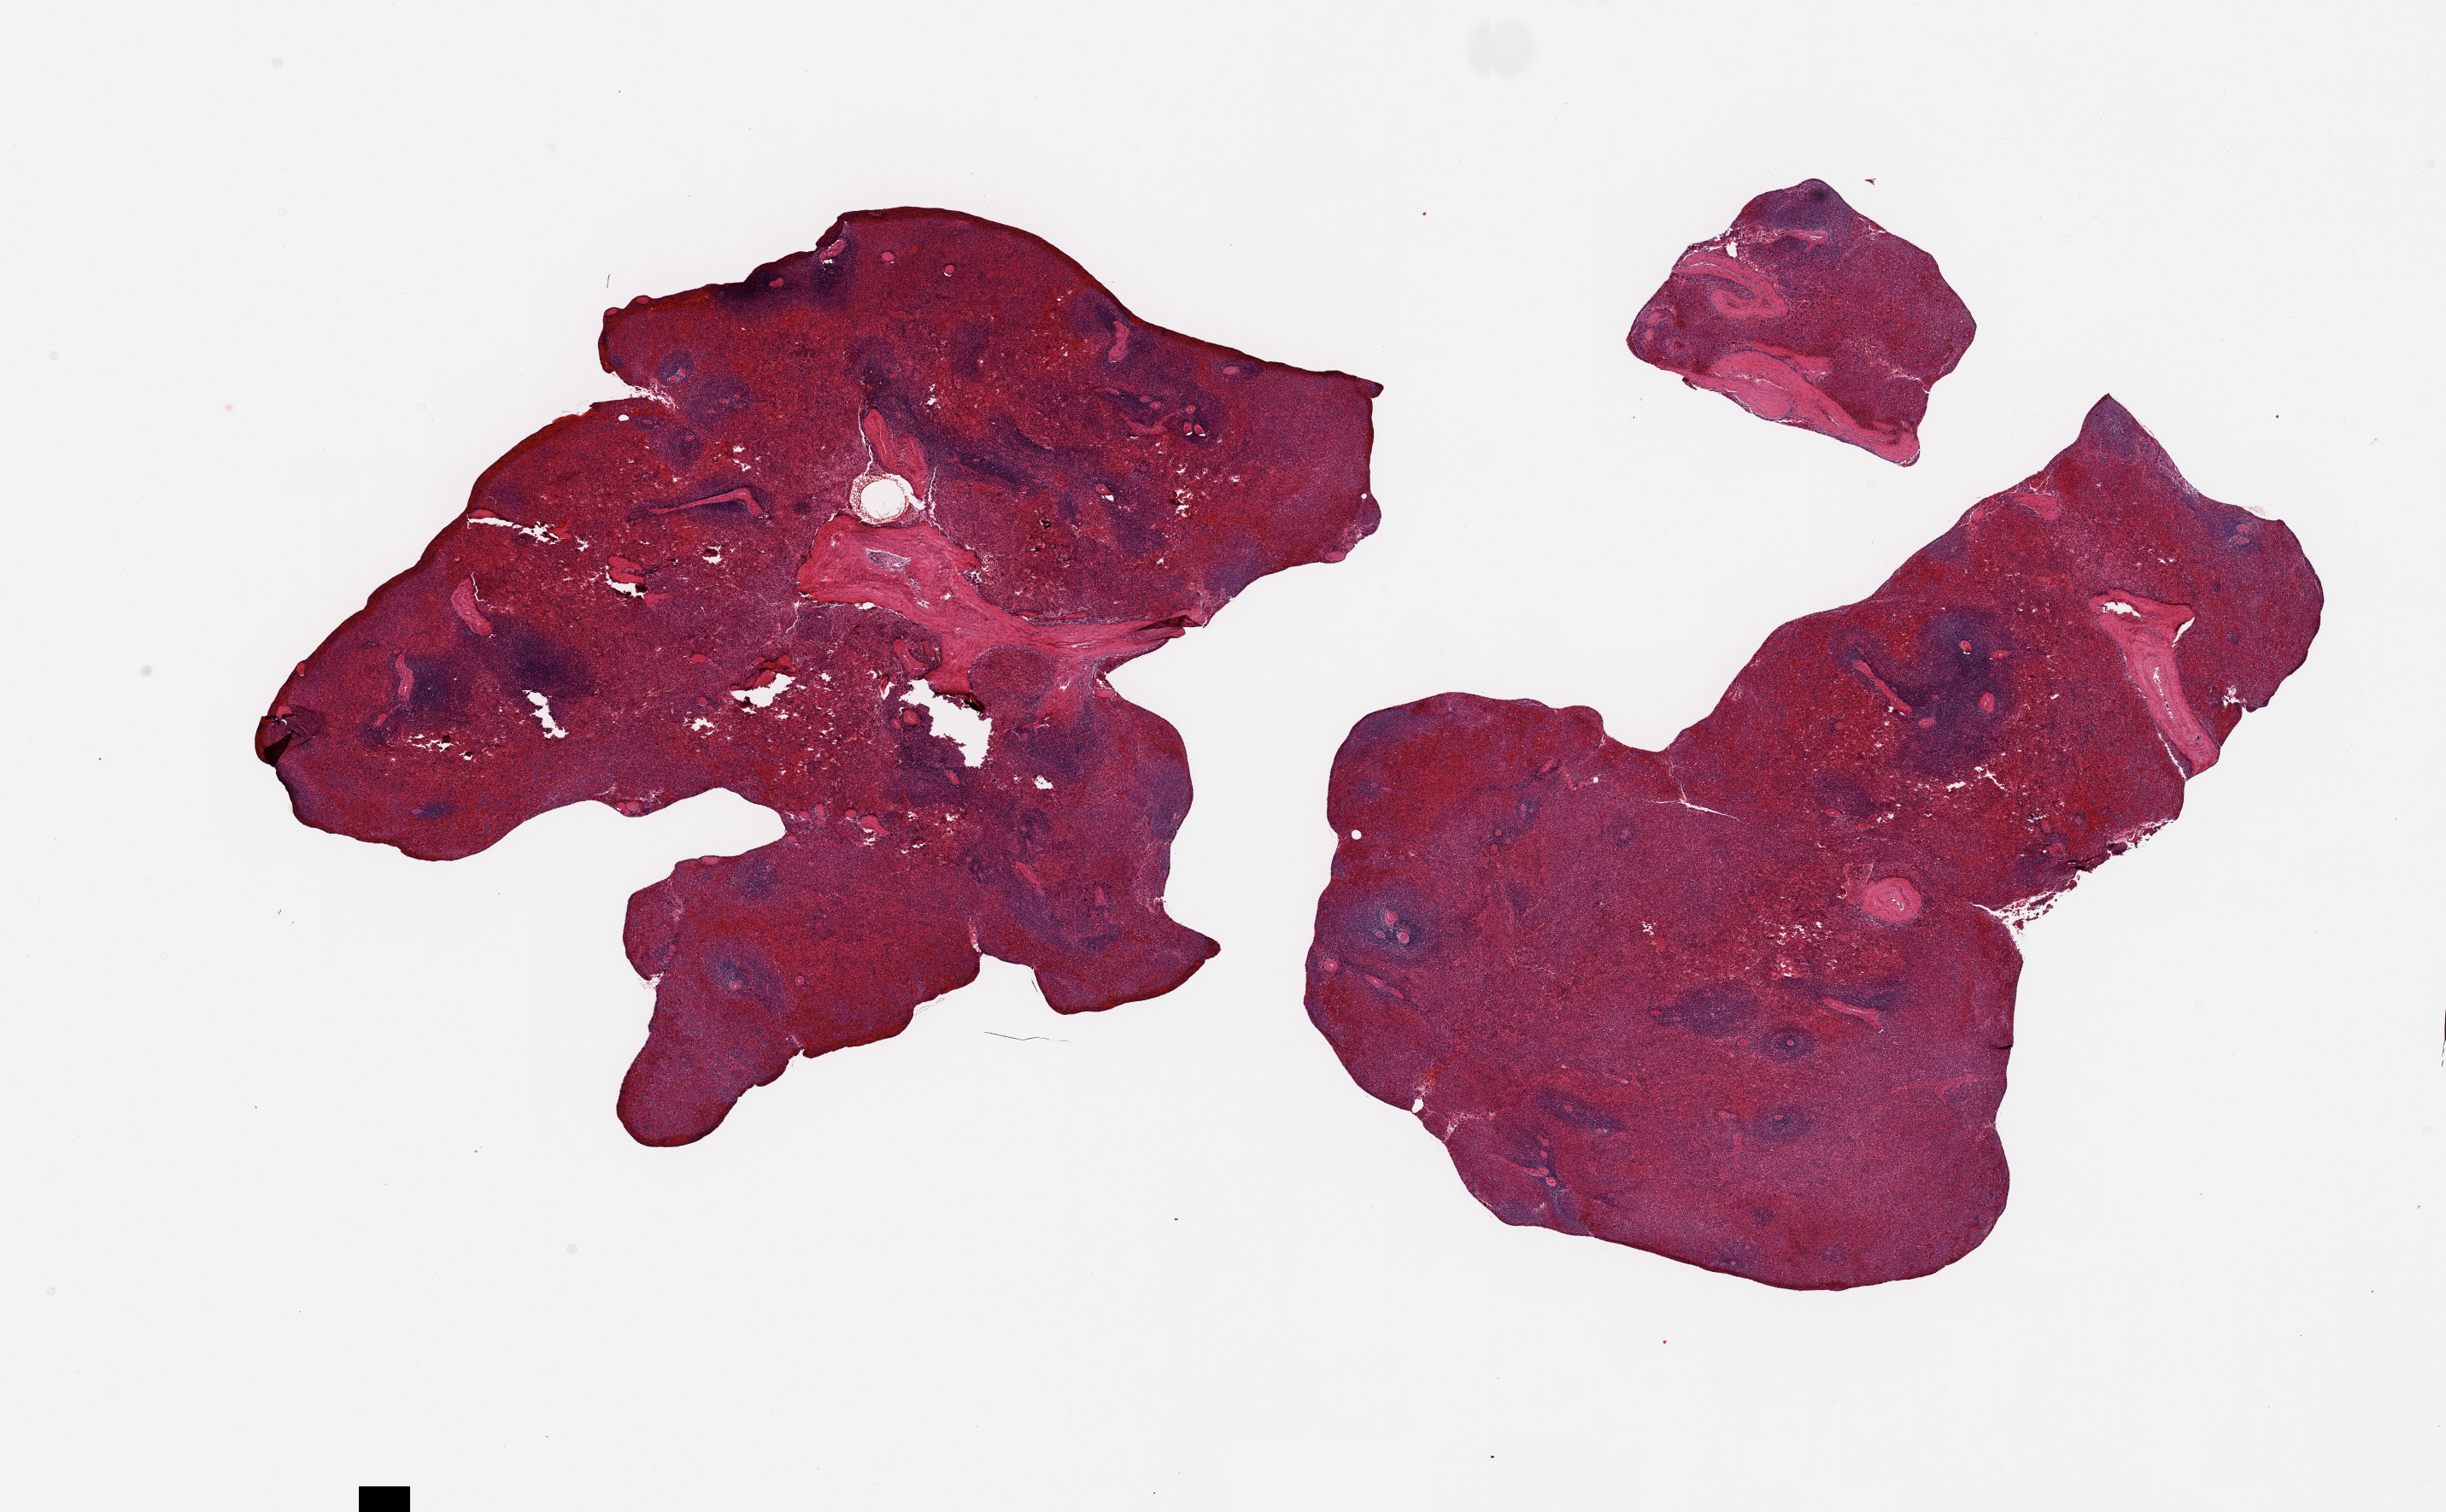
Digitized haematoxylin and eosin-stained section, low-resolution overview of the scanned area, about 22.6 x 14.0 mm (acquisition: 20x scan); PAXgene-fixed paraffin-embedded (PFPE) section; target tissue: spleen; tissue donor sample. Female donor.
- reviewer comment on this tissue sample: 2 pieces; moderate congestion